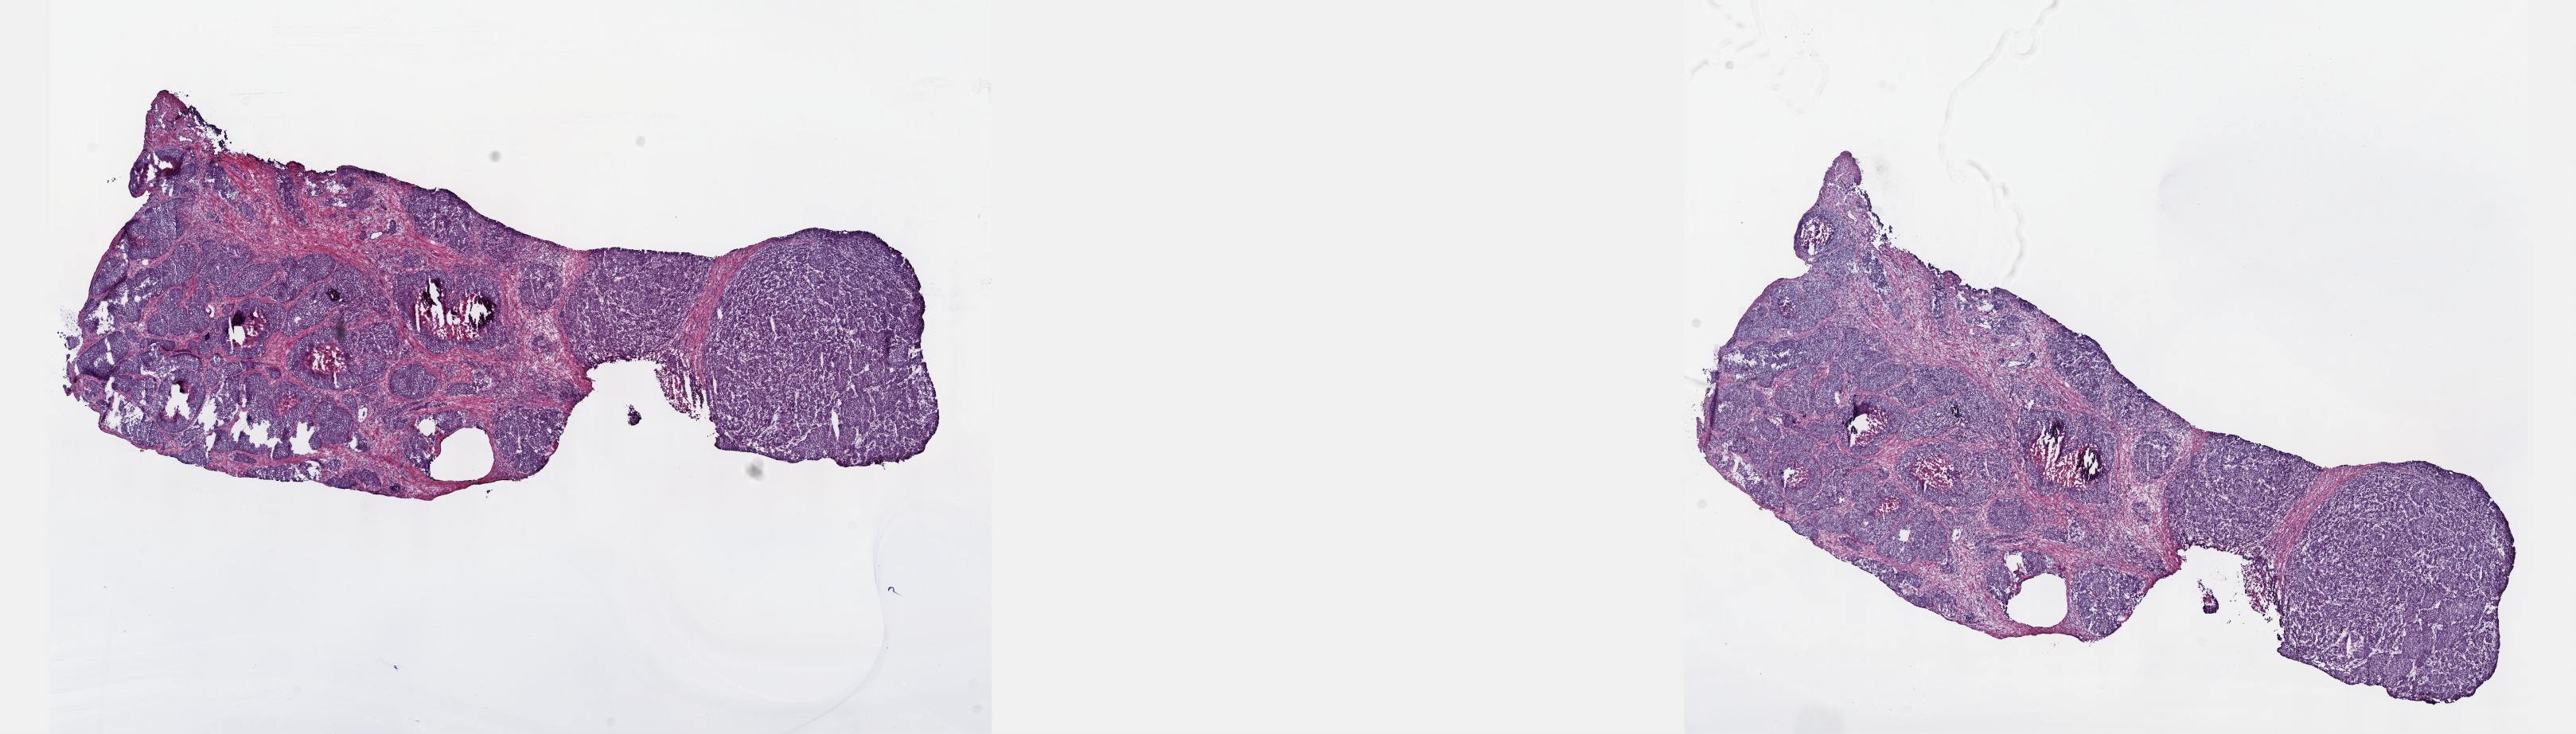
Hematoxylin and eosin (H&E) stained whole-slide image — shown as a low-resolution overview of the whole scanned area (about 26.2 x 7.4 mm, from a 40x scan); frozen section from the top of the tissue portion; sample: primary tumour, prostate. Patient: male, age at initial diagnosis 78 years. Gleason score: 9 (5+4). Slide review estimates, as recorded: tumour cells 75%, tumour nuclei 80%, normal cells 0%, stromal cells 25%, necrosis 0%. Inflammatory infiltration, as recorded: lymphocyte infiltration 0%, monocyte infiltration 0%, neutrophil infiltration 0%.
Pathologic diagnosis: Adenocarcinoma, NOS (prostate gland).